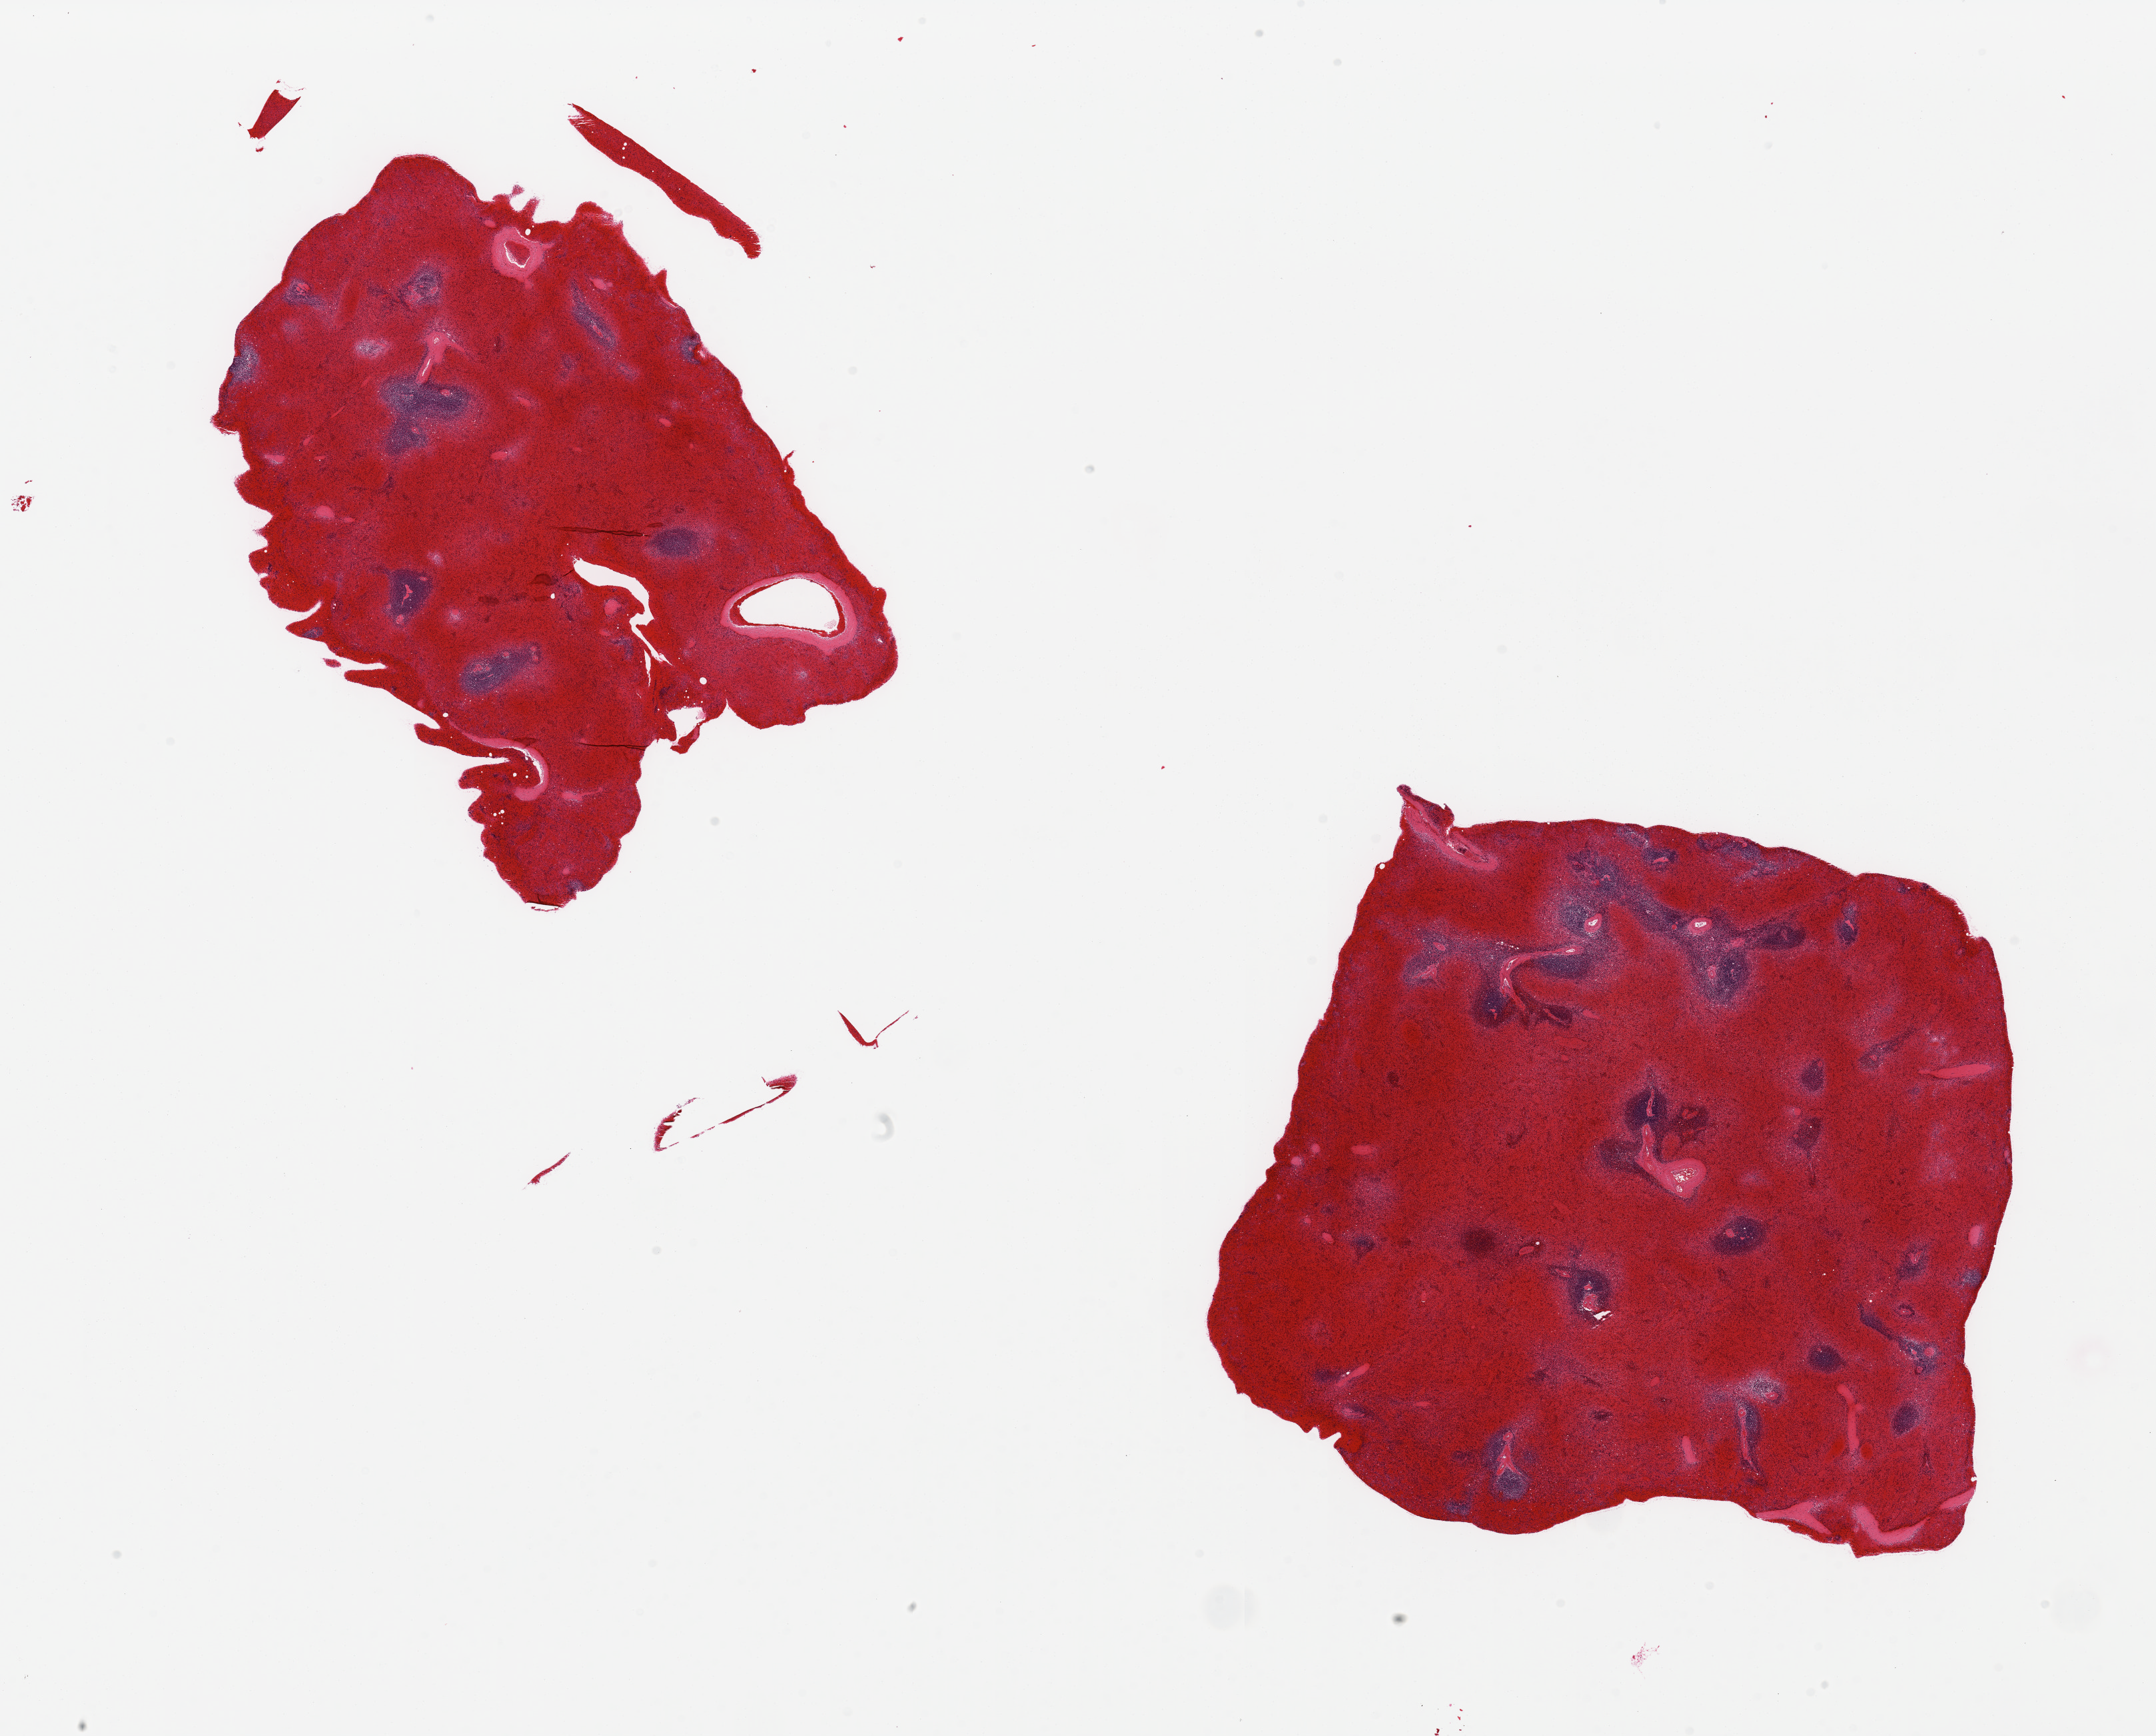
Whole-slide image, haematoxylin and eosin stain, low-resolution overview of the scanned area, about 25.6 x 20.6 mm (acquisition: 20x scan); PAXgene-fixed paraffin-embedded (PFPE) section; target tissue: spleen; donor tissue sample. Donor: male.
Reviewer comment on this tissue sample: 2 pieces, marked congestion.